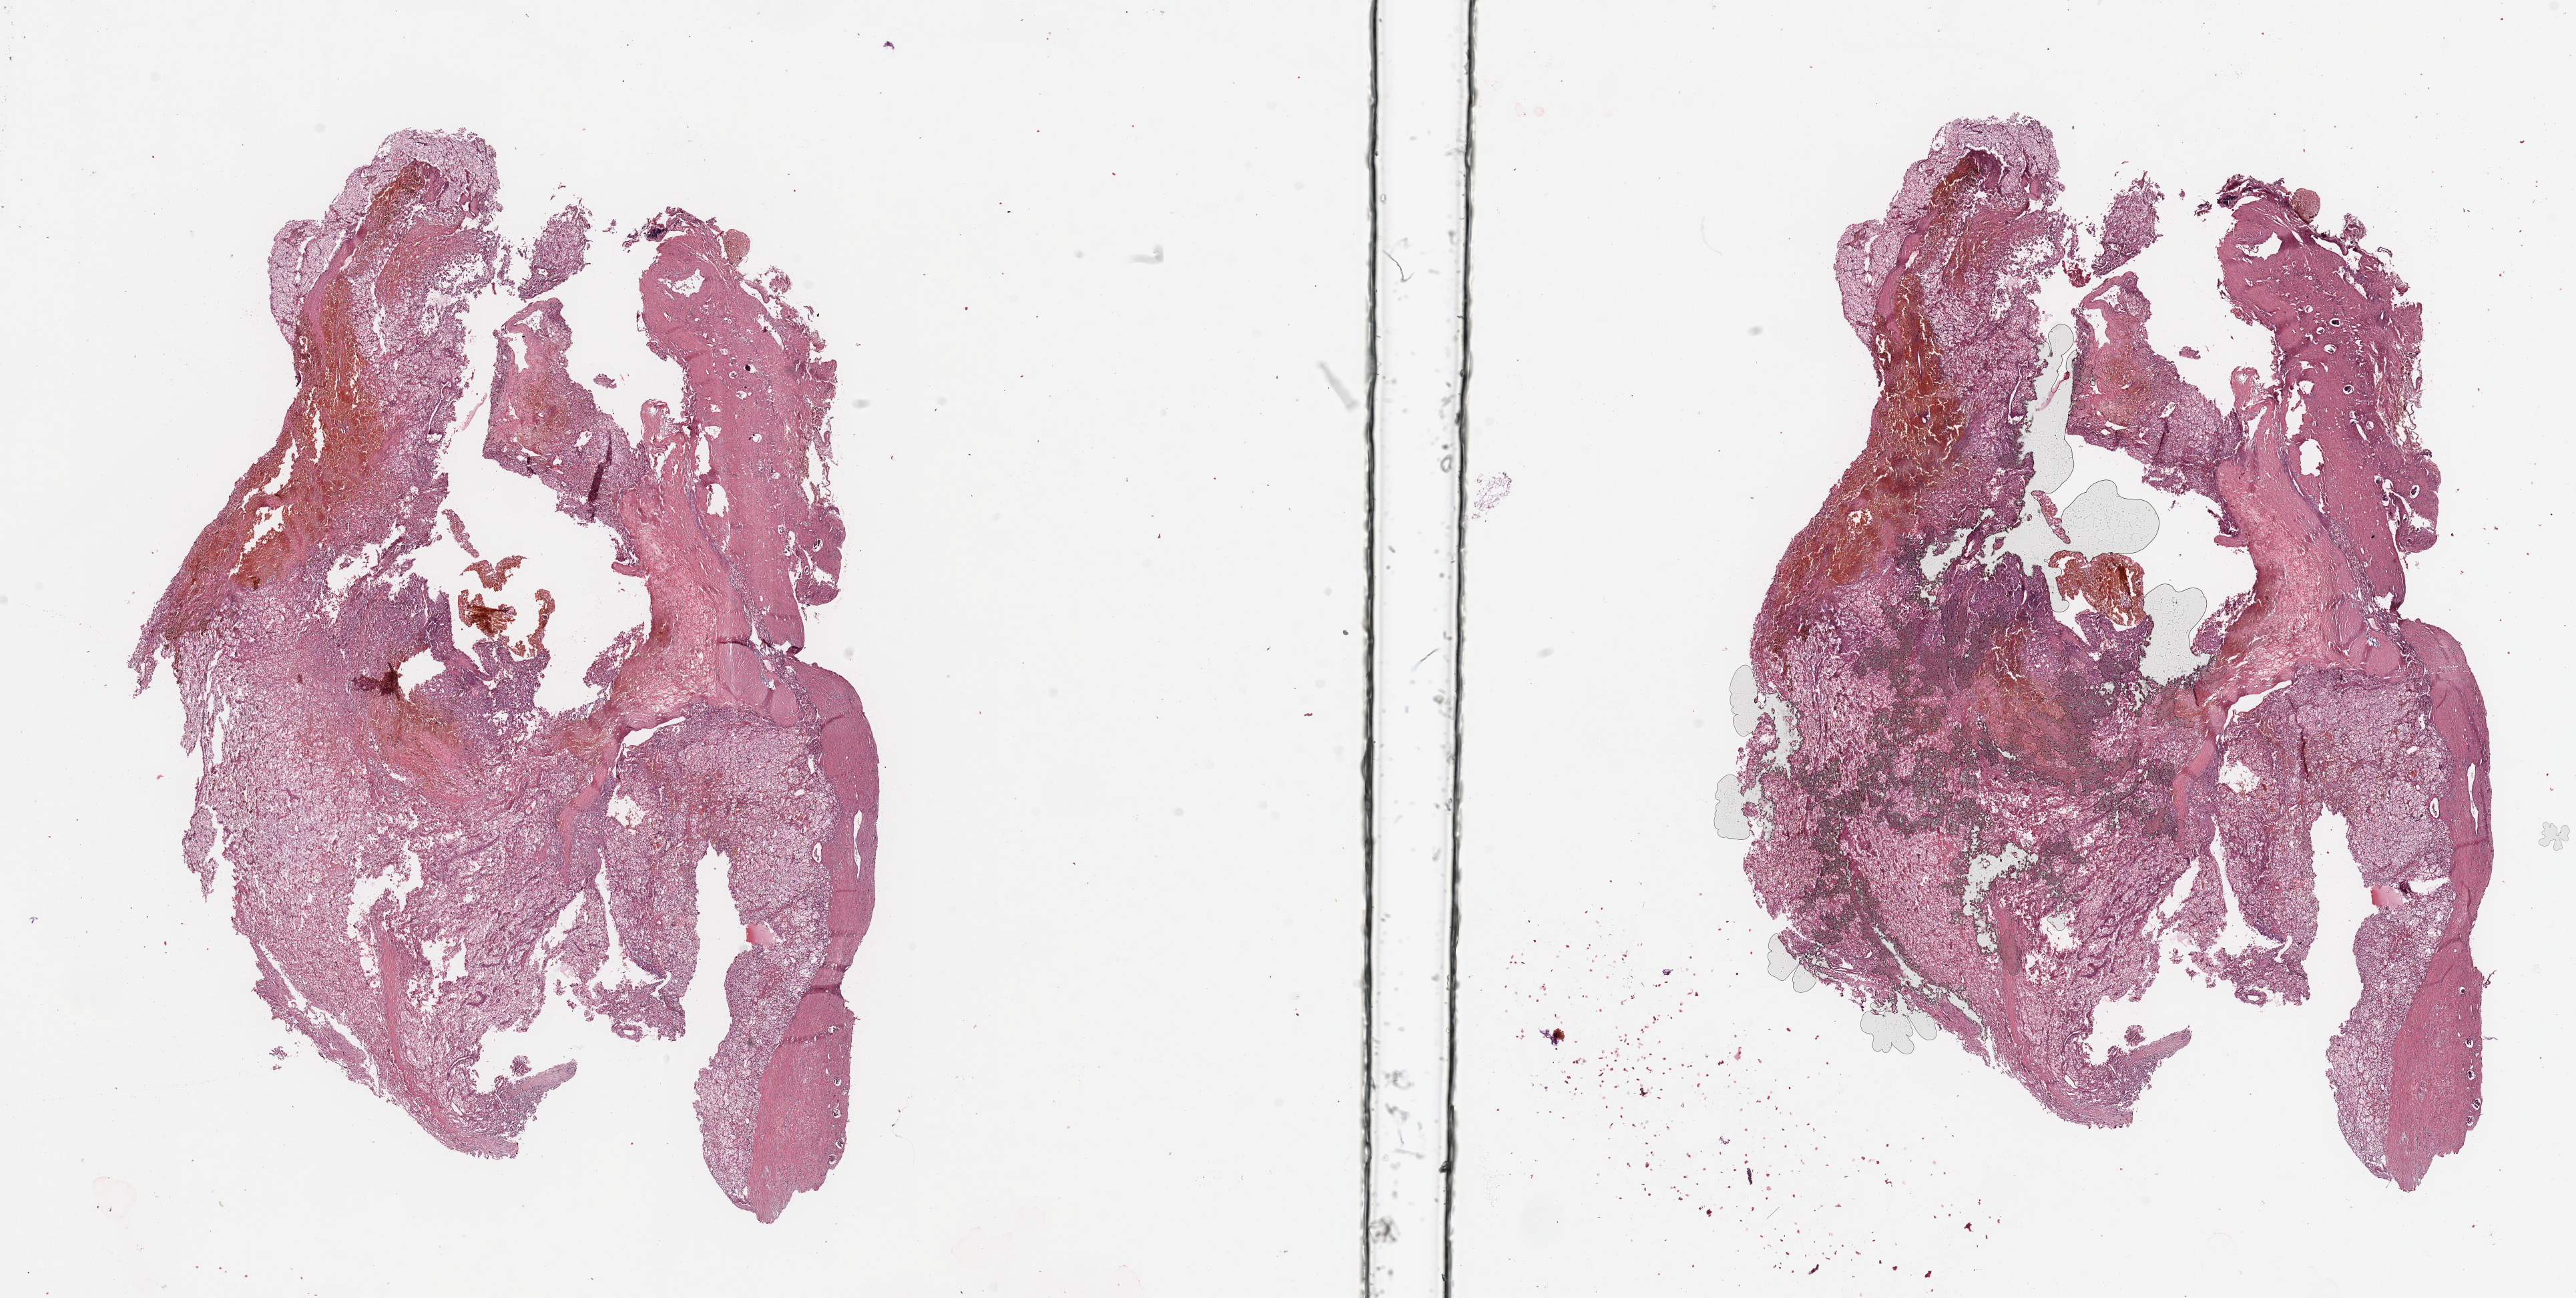
Digitized Hematoxylin and eosin (H&E) stained tissue section (whole slide) — shown as a low-resolution overview of the whole scanned area (about 30.5 x 15.4 mm, slide scanned at 20x). Tumour tissue sample, kidney. Male, 58 y/o. Histologic grade: G2 (moderately differentiated).
Histologic diagnosis: Renal cell carcinoma, NOS. AJCC pathologic stage: III.